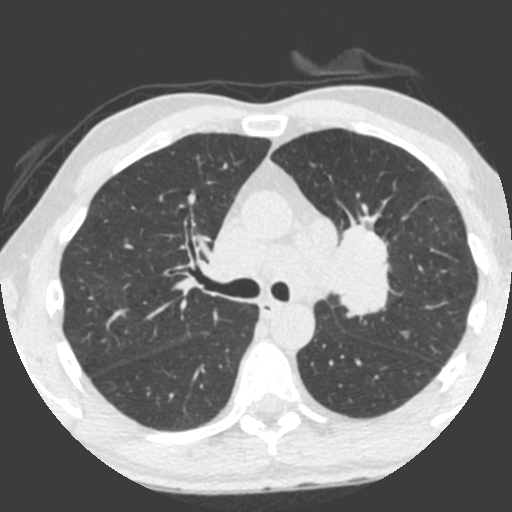
Low-dose screening chest CT, one axial slice. Slice 142 of 212 in the series (ordered by position). Lung window (W 1500 / L -600 HU). 2 mm slice thickness. 512 × 512 image matrix, field of view 315 × 315 mm.
Annotated regions visible in this slice (expert manual segmentation):
- lesion 1 (tumor, upper lobe of left lung): bounding box <330,224,390,319> (left, top, right, bottom; pixels)